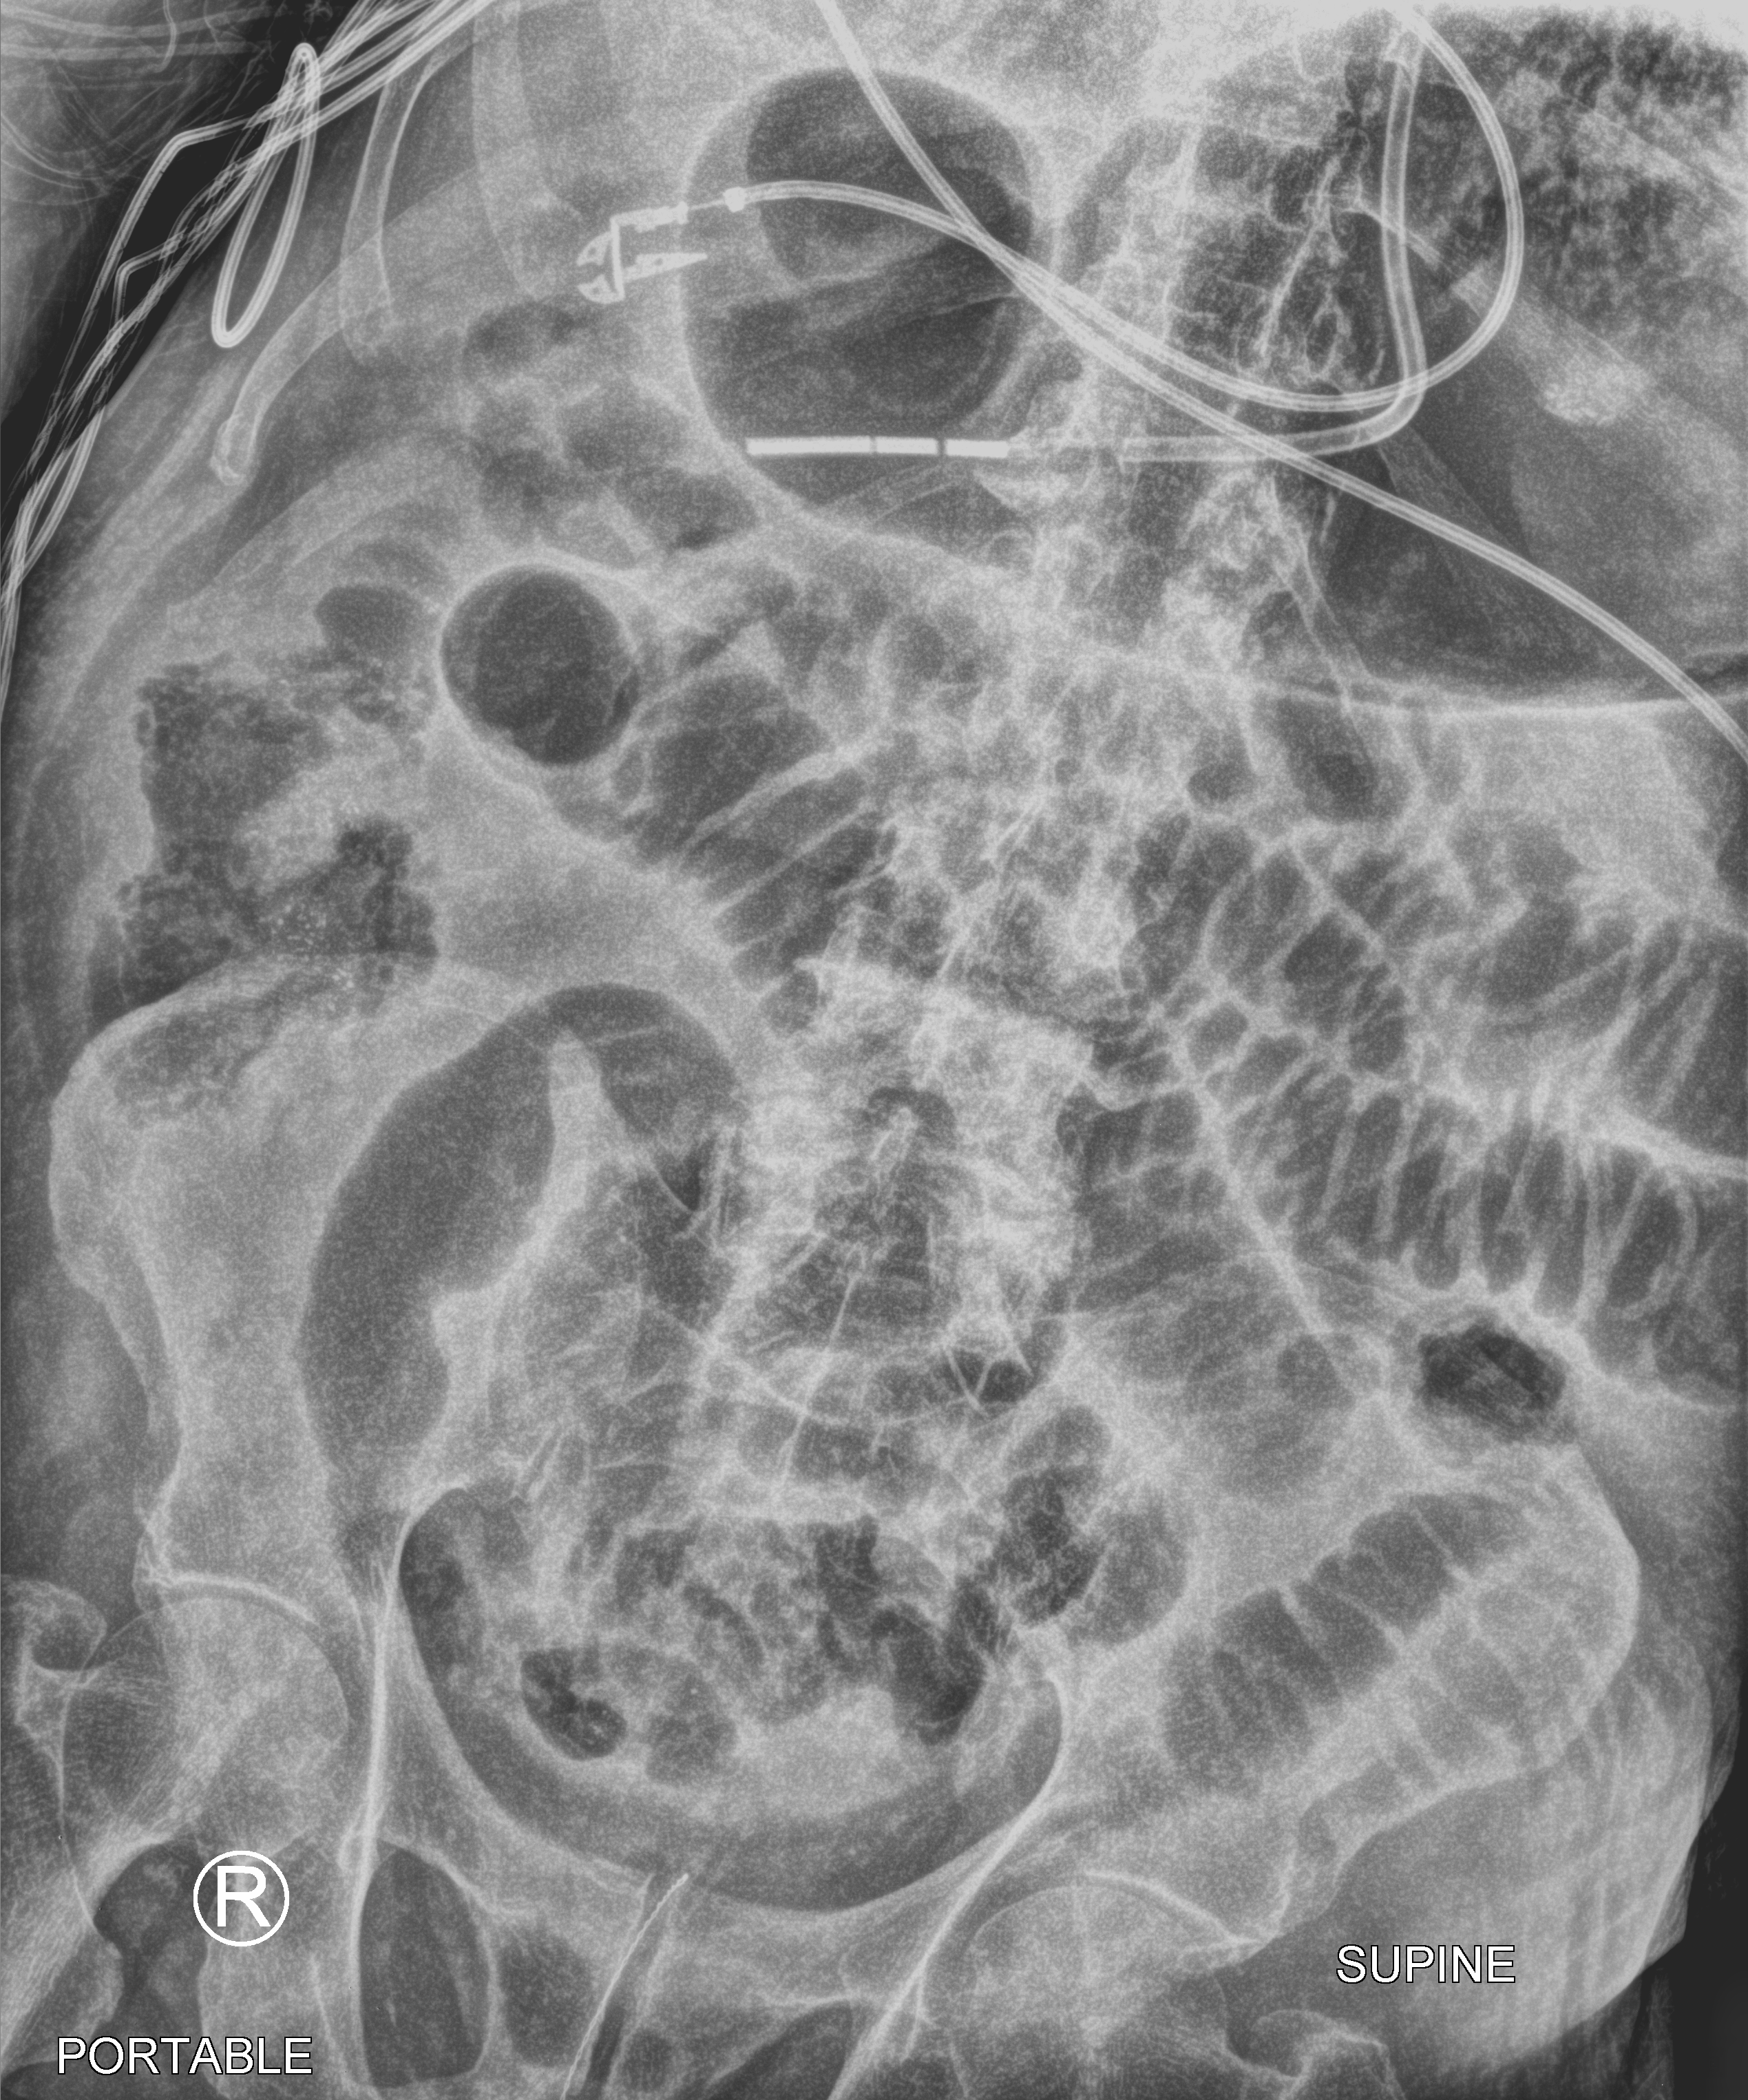
Bedside abdomen radiograph (computed radiography), anteroposterior (AP) projection. Patient hospitalised with COVID-19; male, aged 75–90 years.
From the hospital-stay record, not from the radiograph (when in the stay this image was taken is not recorded): mechanically ventilated during this hospital stay: yes; admitted to intensive care during this hospital stay: yes; length of hospital stay: 26 days.